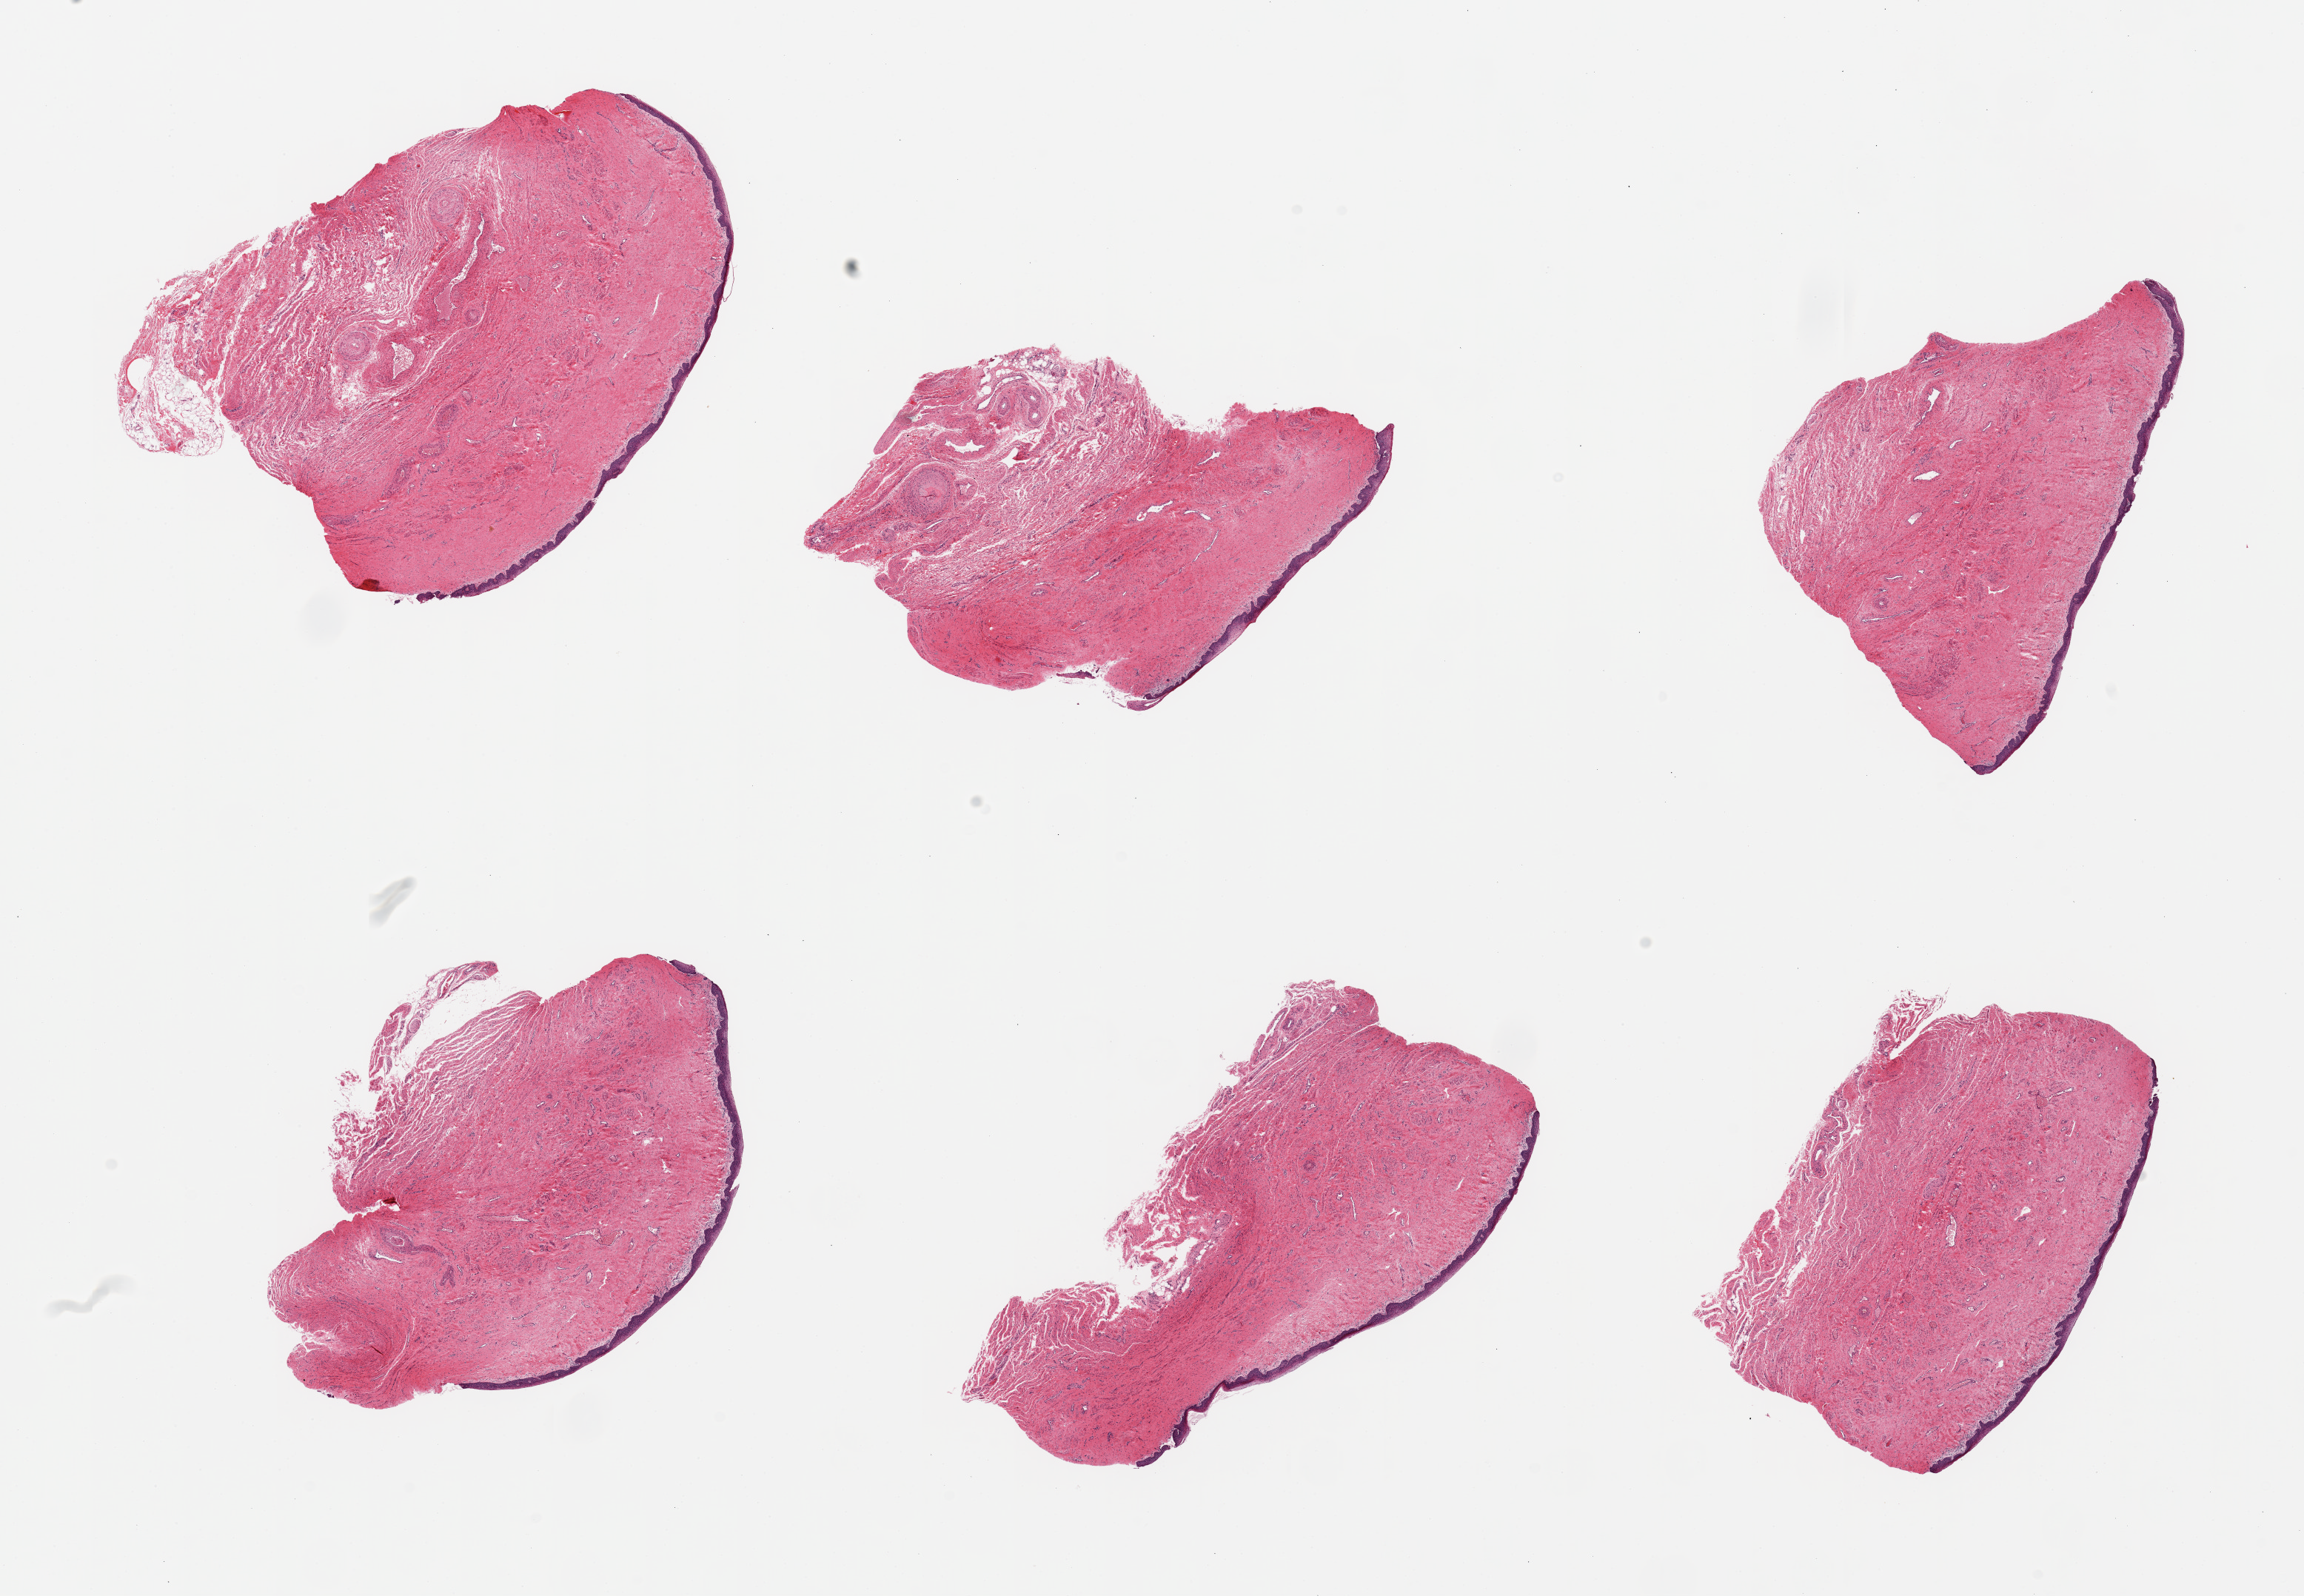
Digitized hematoxylin and eosin (H&E)-stained section, brightfield, whole scanned area (about 24.6 x 17.1 mm, slide scanned at 20x) shown as a low-resolution overview; PAXgene-fixed paraffin-embedded (PFPE) section; sampled site (target tissue): vagina; tissue donor sample. Donor sex: female.
Reviewer comment on this tissue sample: 6 pieces, squamous mucosa up to~130 microns.